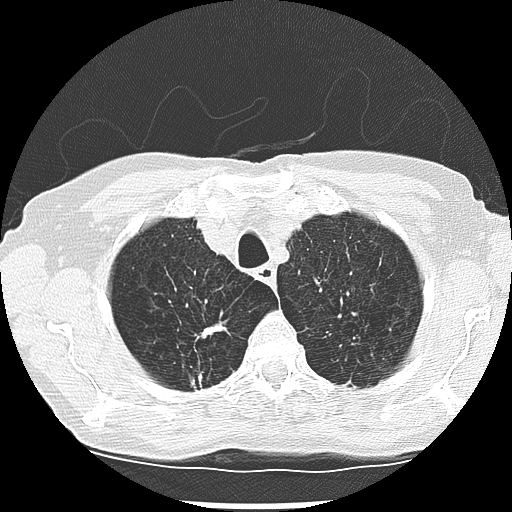
Low-dose screening chest CT, one axial slice. Position 229 of 265 along the scan axis. Reconstruction kernel LUNG. Lung window (W 1500 / L -600 HU). 2.5 mm slice thickness. 512 × 512 image matrix, field of view 300 × 300 mm.
Structures marked on this image (outlined manually by an expert reader):
- lesion 1 (nodule, upper lobe of right lung): bounding box <198,377,202,378> (left, top, right, bottom; pixels)
- lesion 2 (tumor, upper lobe of right lung): <200,323,225,338>